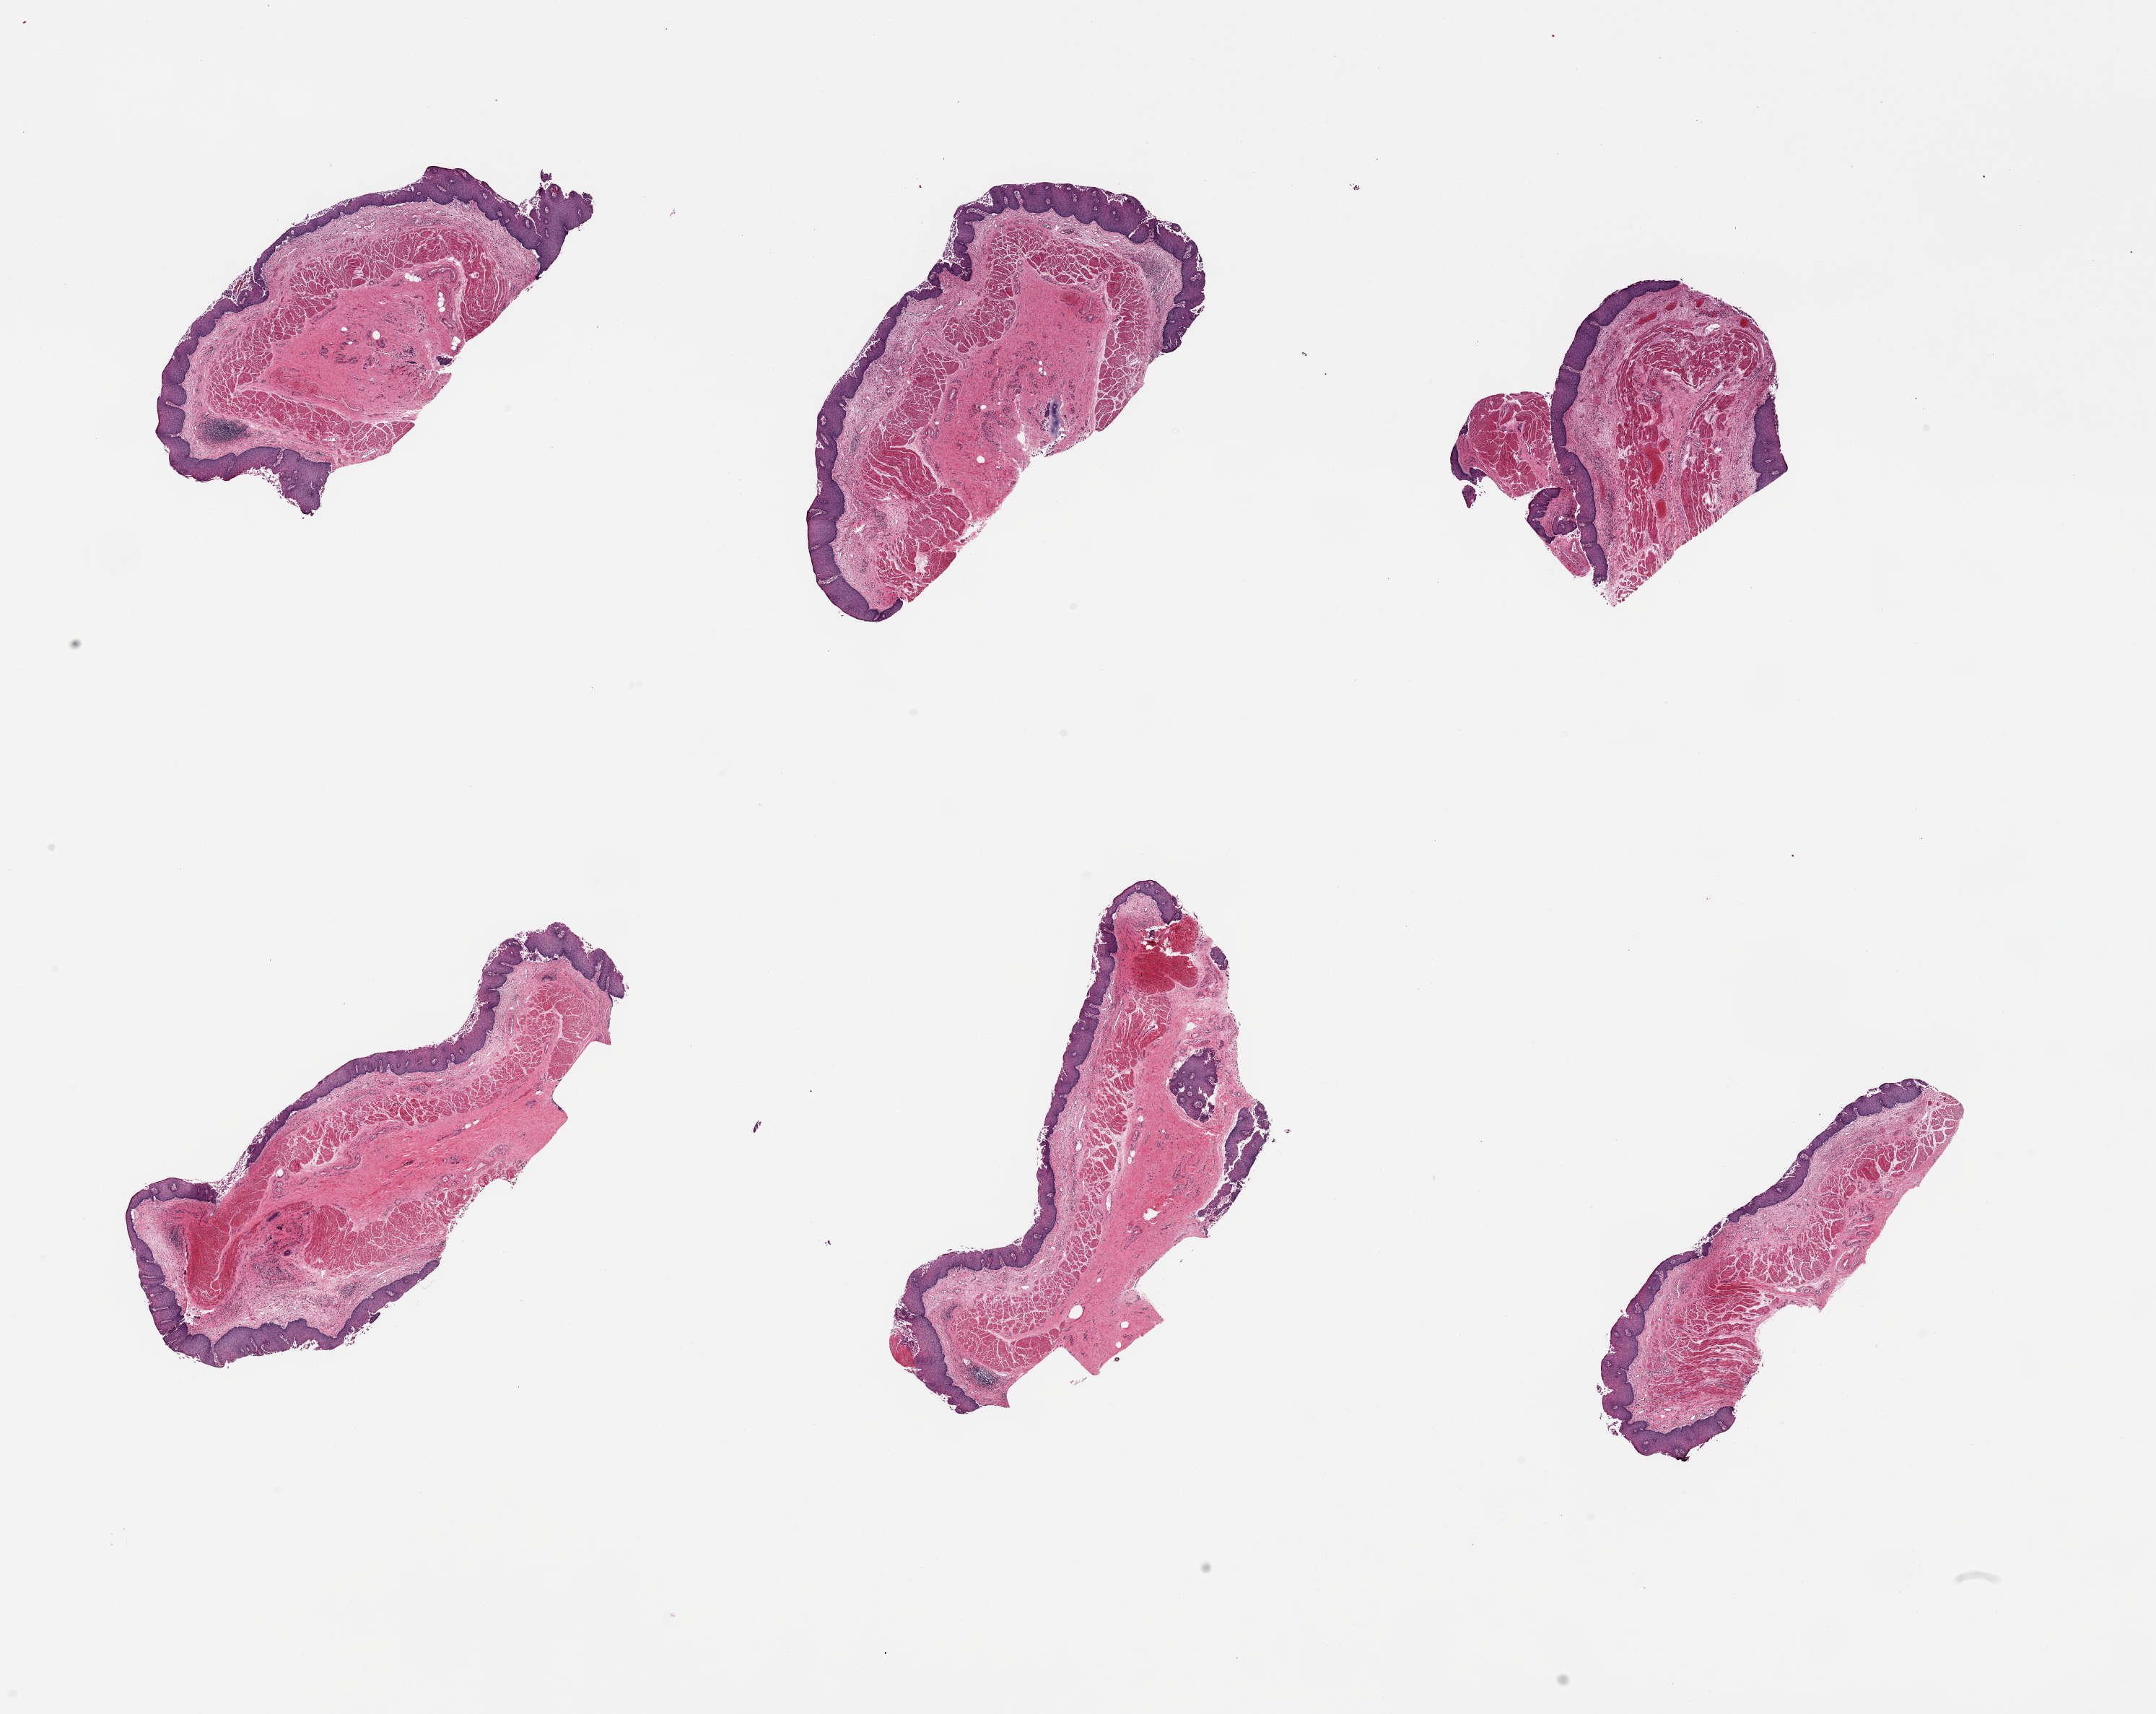
Whole-slide image, haematoxylin and eosin stain, shown as a low-resolution overview of the whole scanned area (about 23.6 x 18.8 mm, acquisition: 20x scan), PAXgene-fixed paraffin-embedded (PFPE) section, sampled site (target tissue): esophageal mucous membrane, tissue donor sample. Male donor.
Reviewer comment on this tissue sample: 6 pieces; one focus of possible submucosal calcification below muscularis.